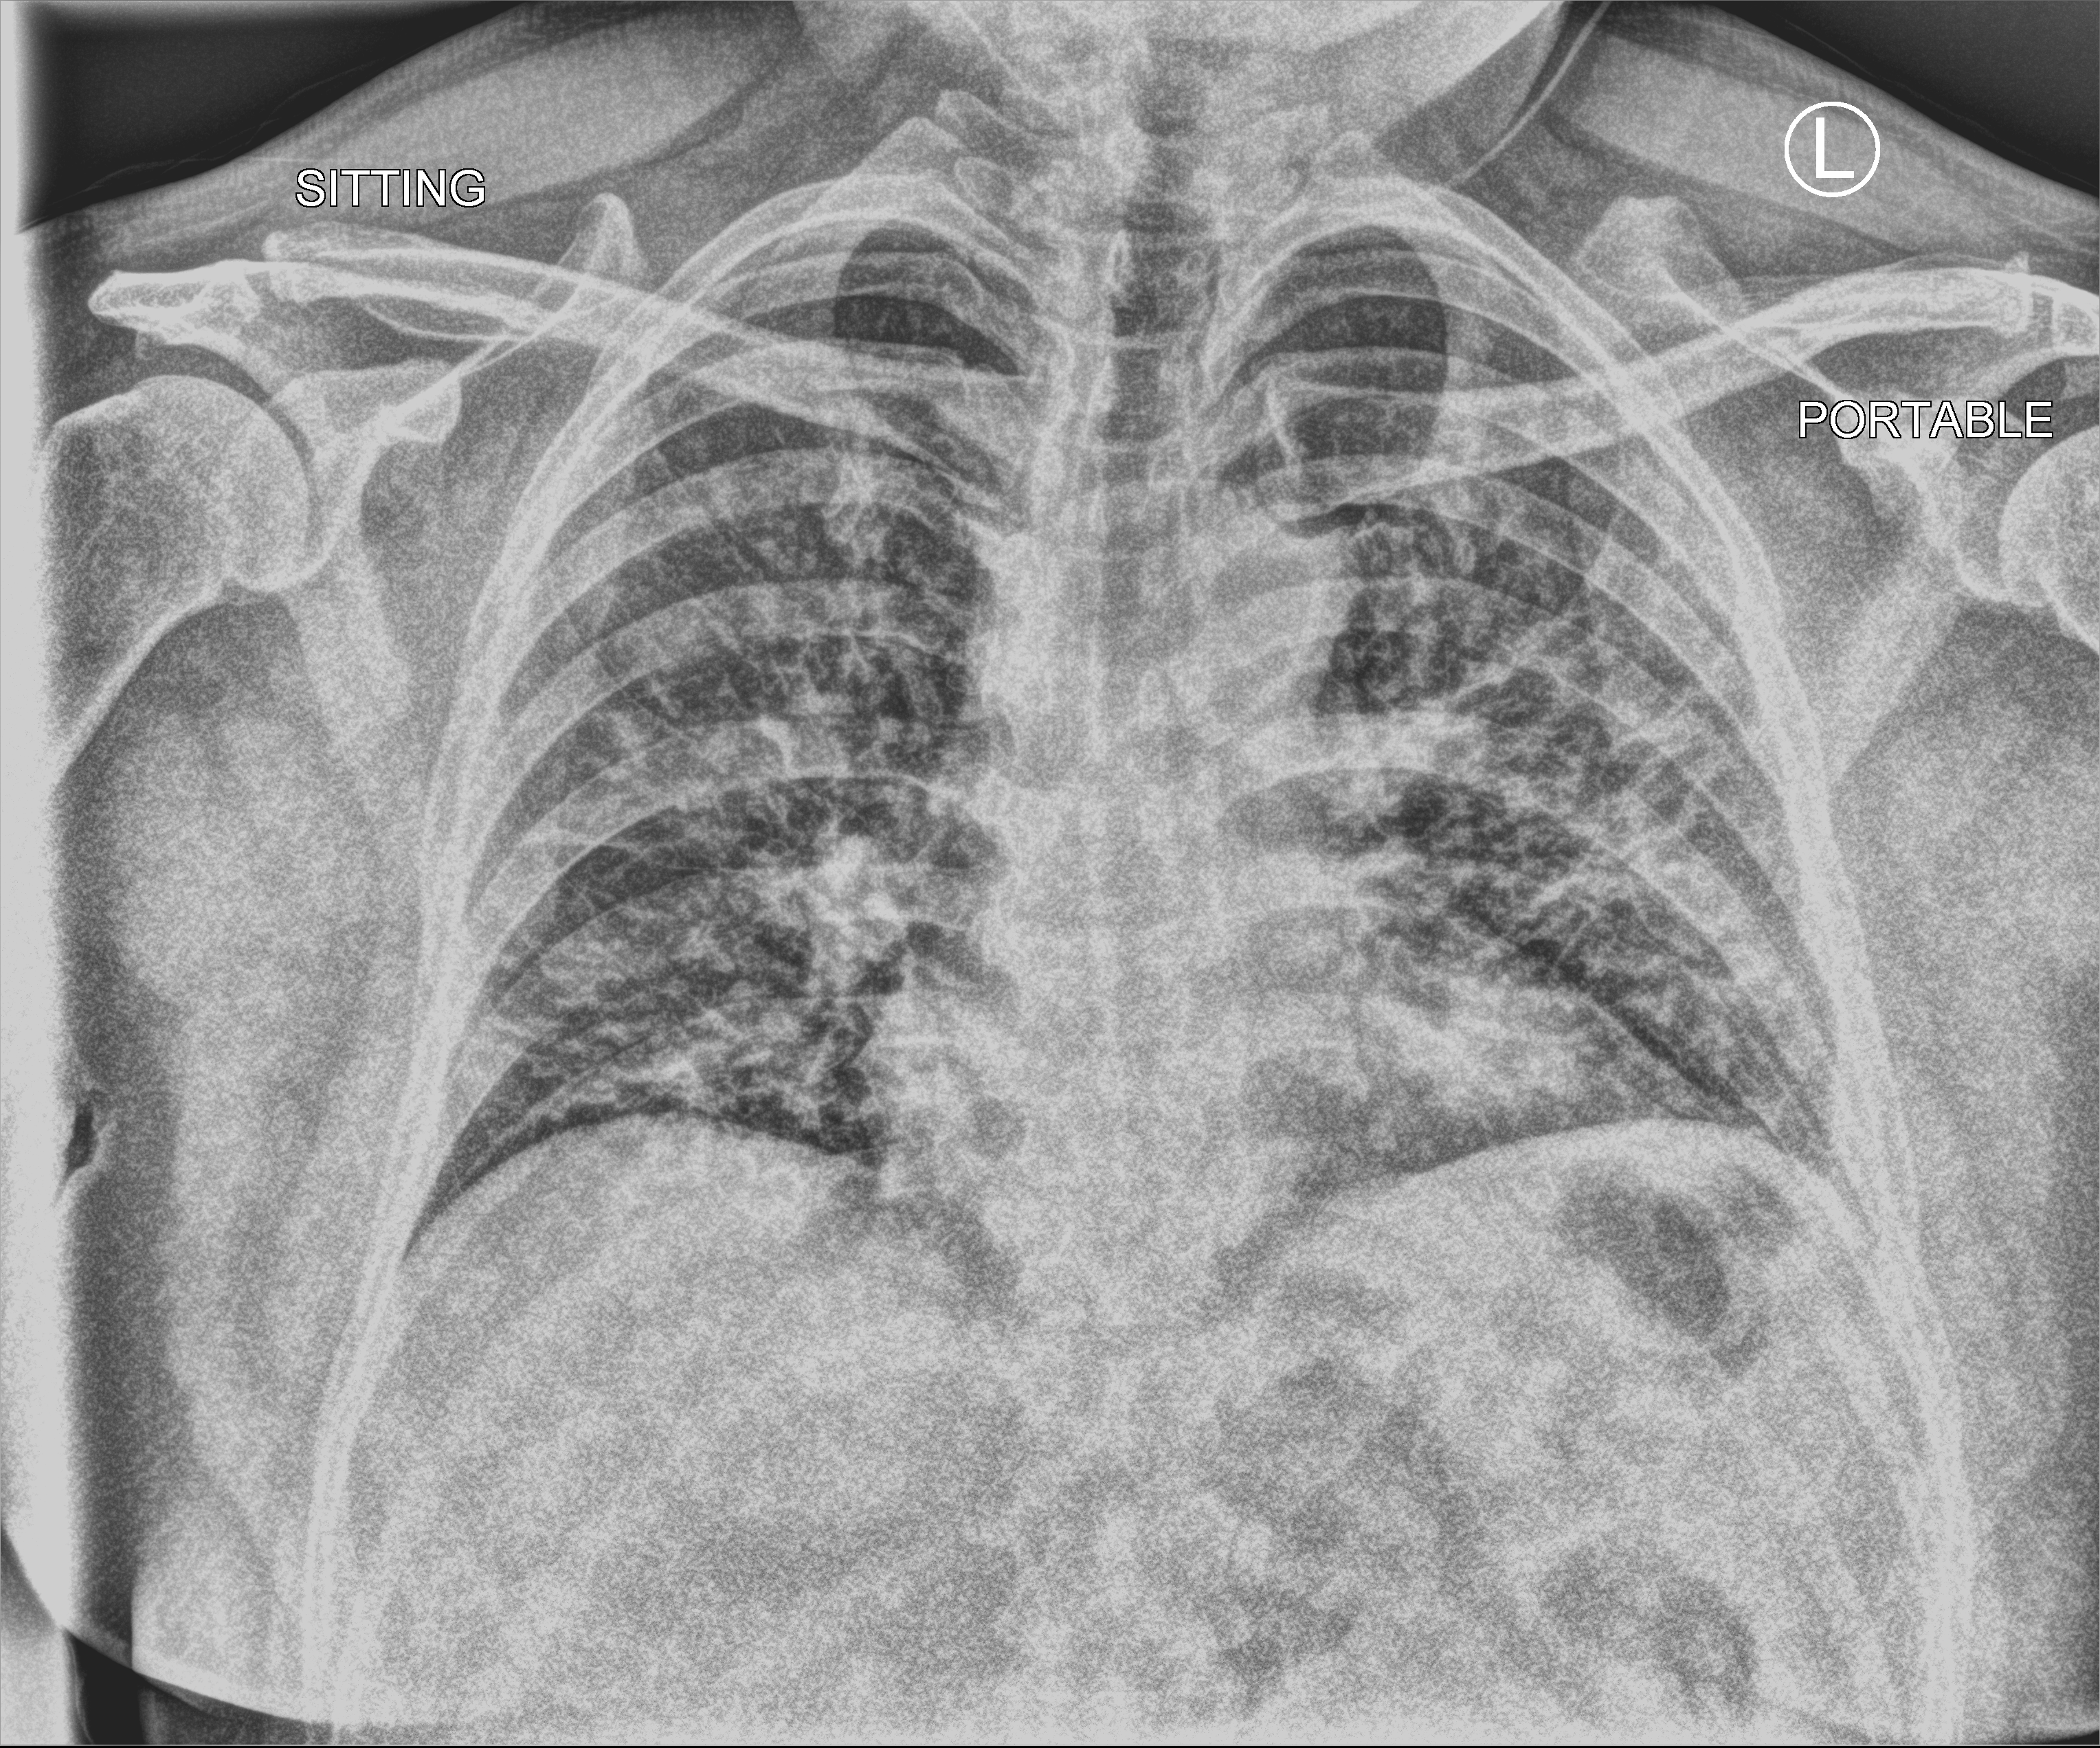
Chest X-ray (portable). Patient hospitalised with COVID-19; male, aged 18–59 years.
Admission-level facts for this patient (not findings on this image; timing relative to this image not recorded): length of hospital stay: 10 days.